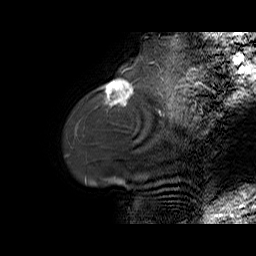
Breast MRI (dynamic contrast-enhanced), one sagittal slice; slice 12 of 70 in the series (ordered by position); dynamic contrast-enhanced series, time point 2 of 6 at this slice position (early post-contrast); 1.5 T; TE 5.5 ms, TR 32.9 ms; 4 mm slice thickness; 256 × 256 image matrix, field of view 240 × 240 mm. Female patient. Case-level facts recorded for this patient, not image findings: setting: breast cancer imaged before/during neoadjuvant chemotherapy; receptor status: HER2-positive.
Structures marked on this image (semi-automatic segmentation, software-assisted and operator-edited):
- analysis volume of interest (the breast-tissue region the enhancement analysis was run in; not a lesion): bounding box <96,80,141,108> (left, top, right, bottom; pixels)
- tumour enhancement mask (voxels above the 100 % enhancement threshold inside the analysis volume of interest): <106,80,133,105>